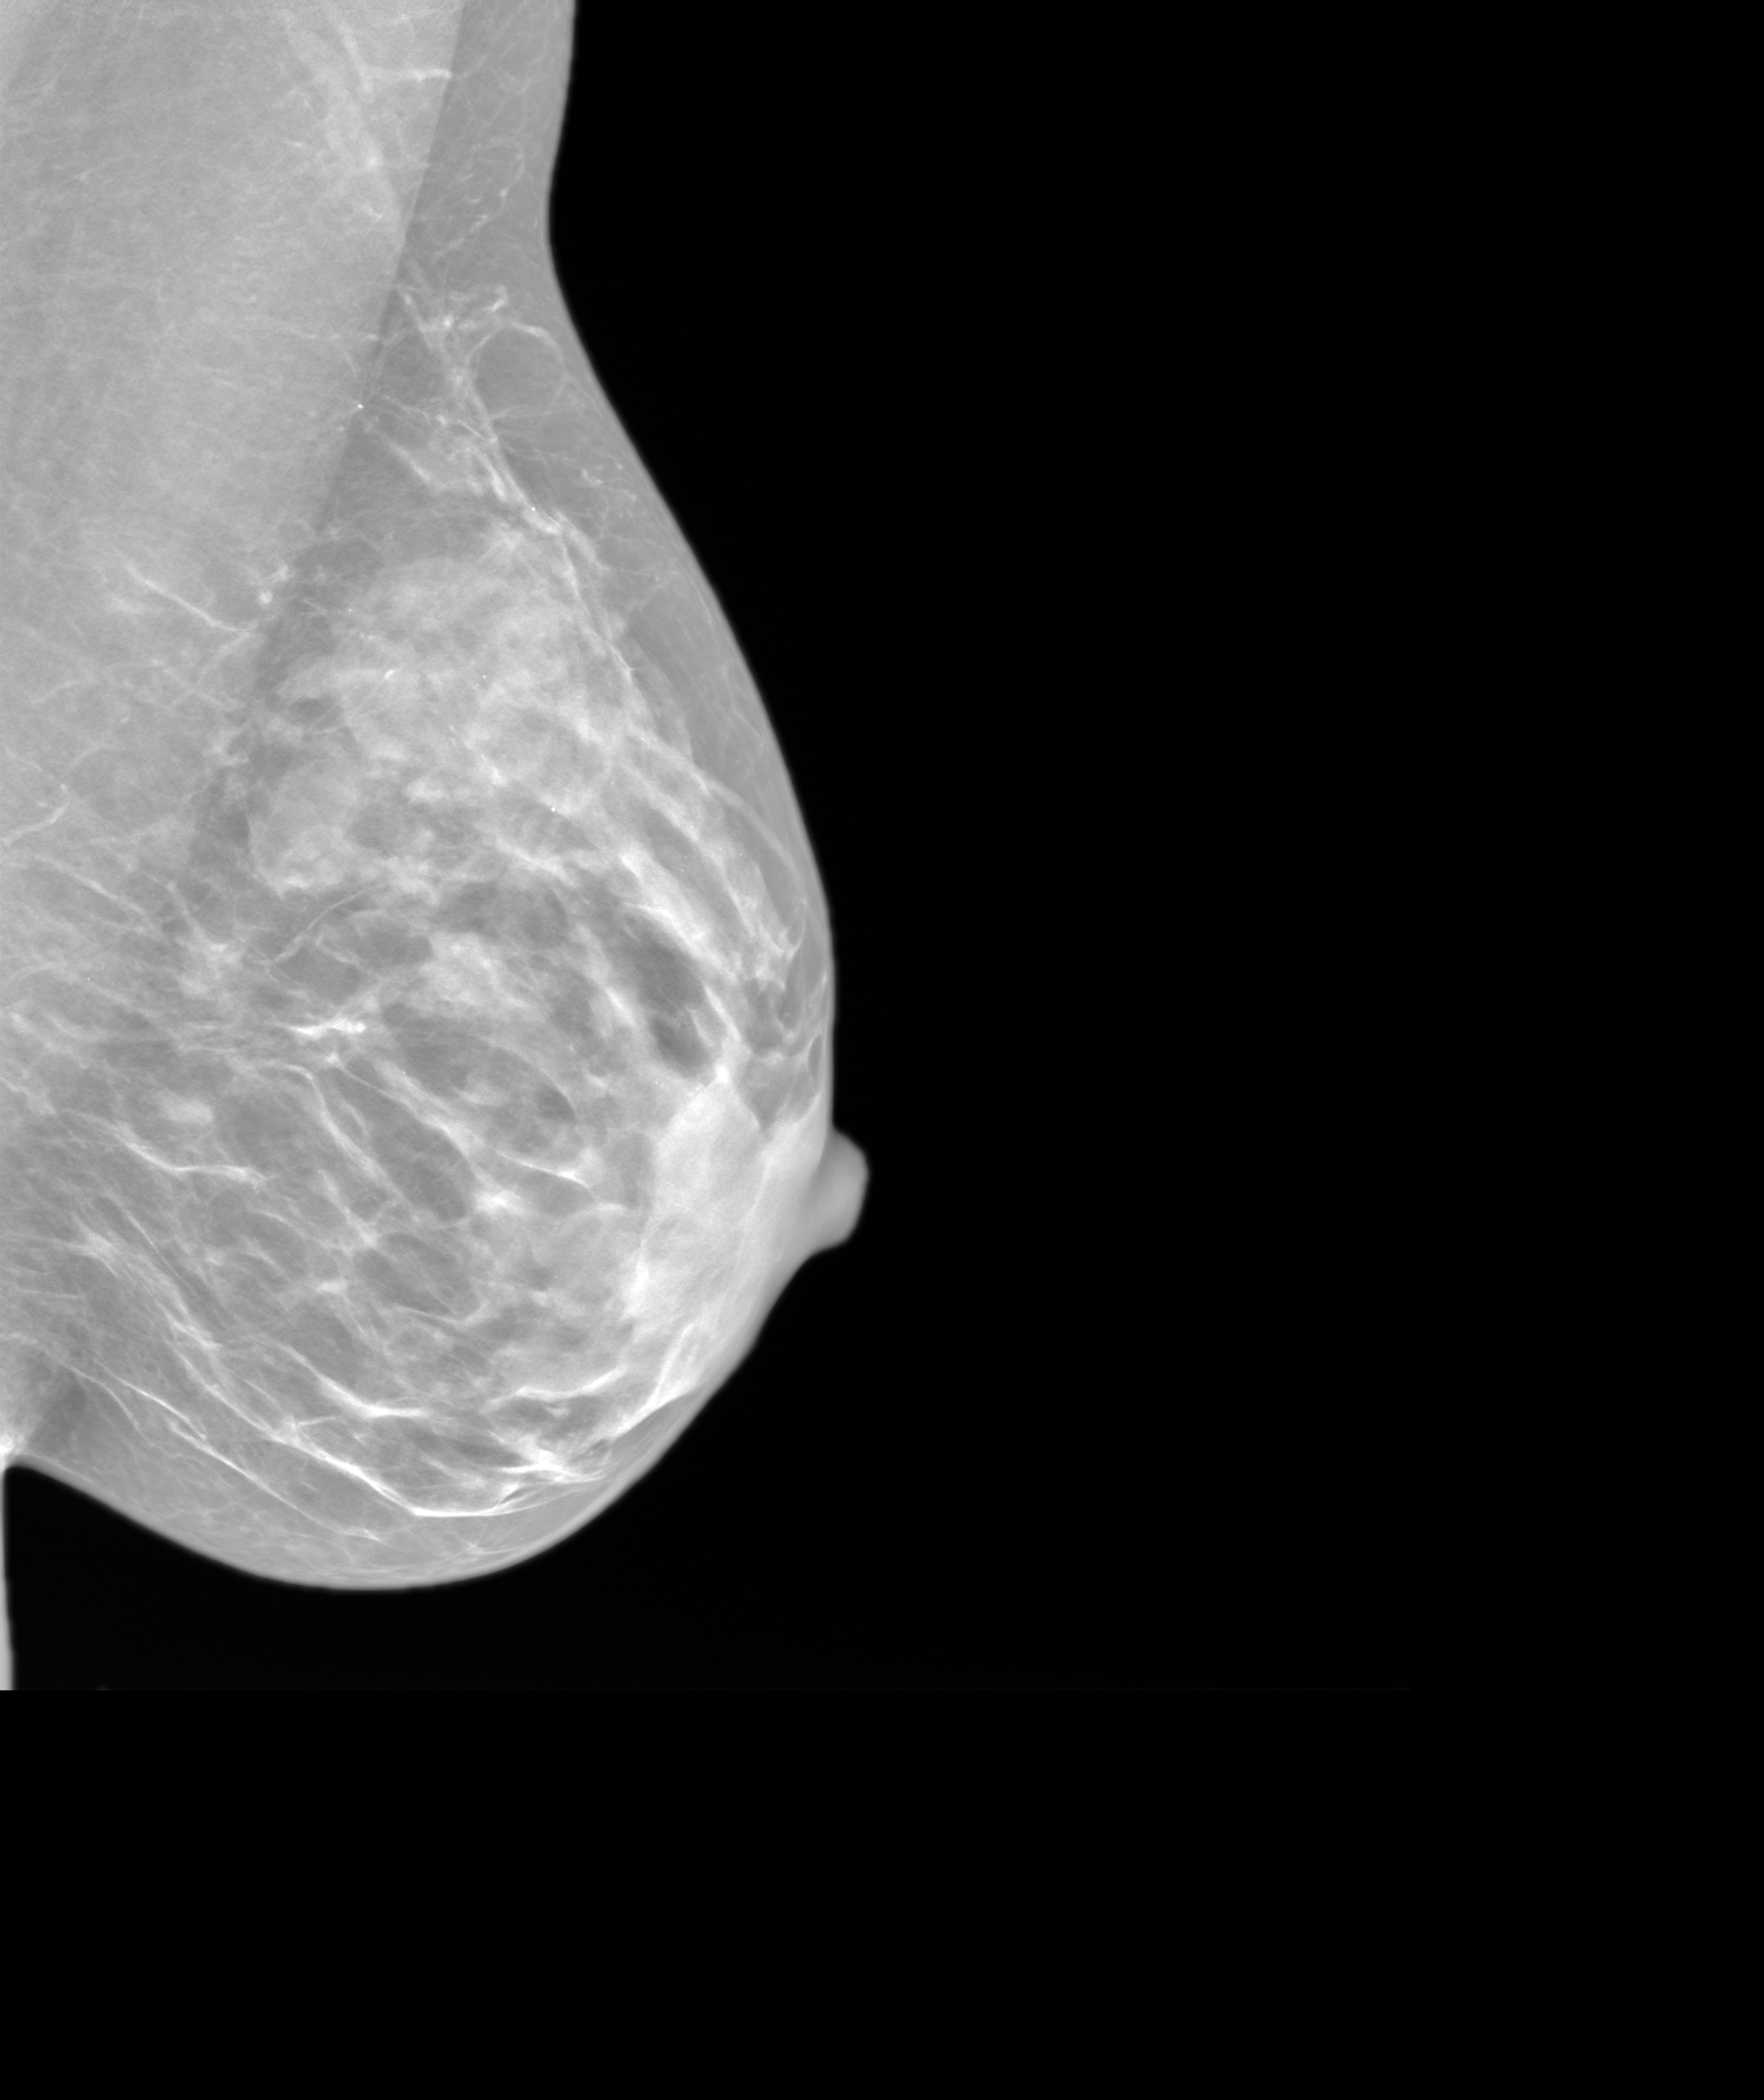
Annual screening mammography examination. Female patient, age 48 years.
Image type: synthesized 2-D view from tomosynthesis. Breast: left. Projection: medio-lateral oblique projection.